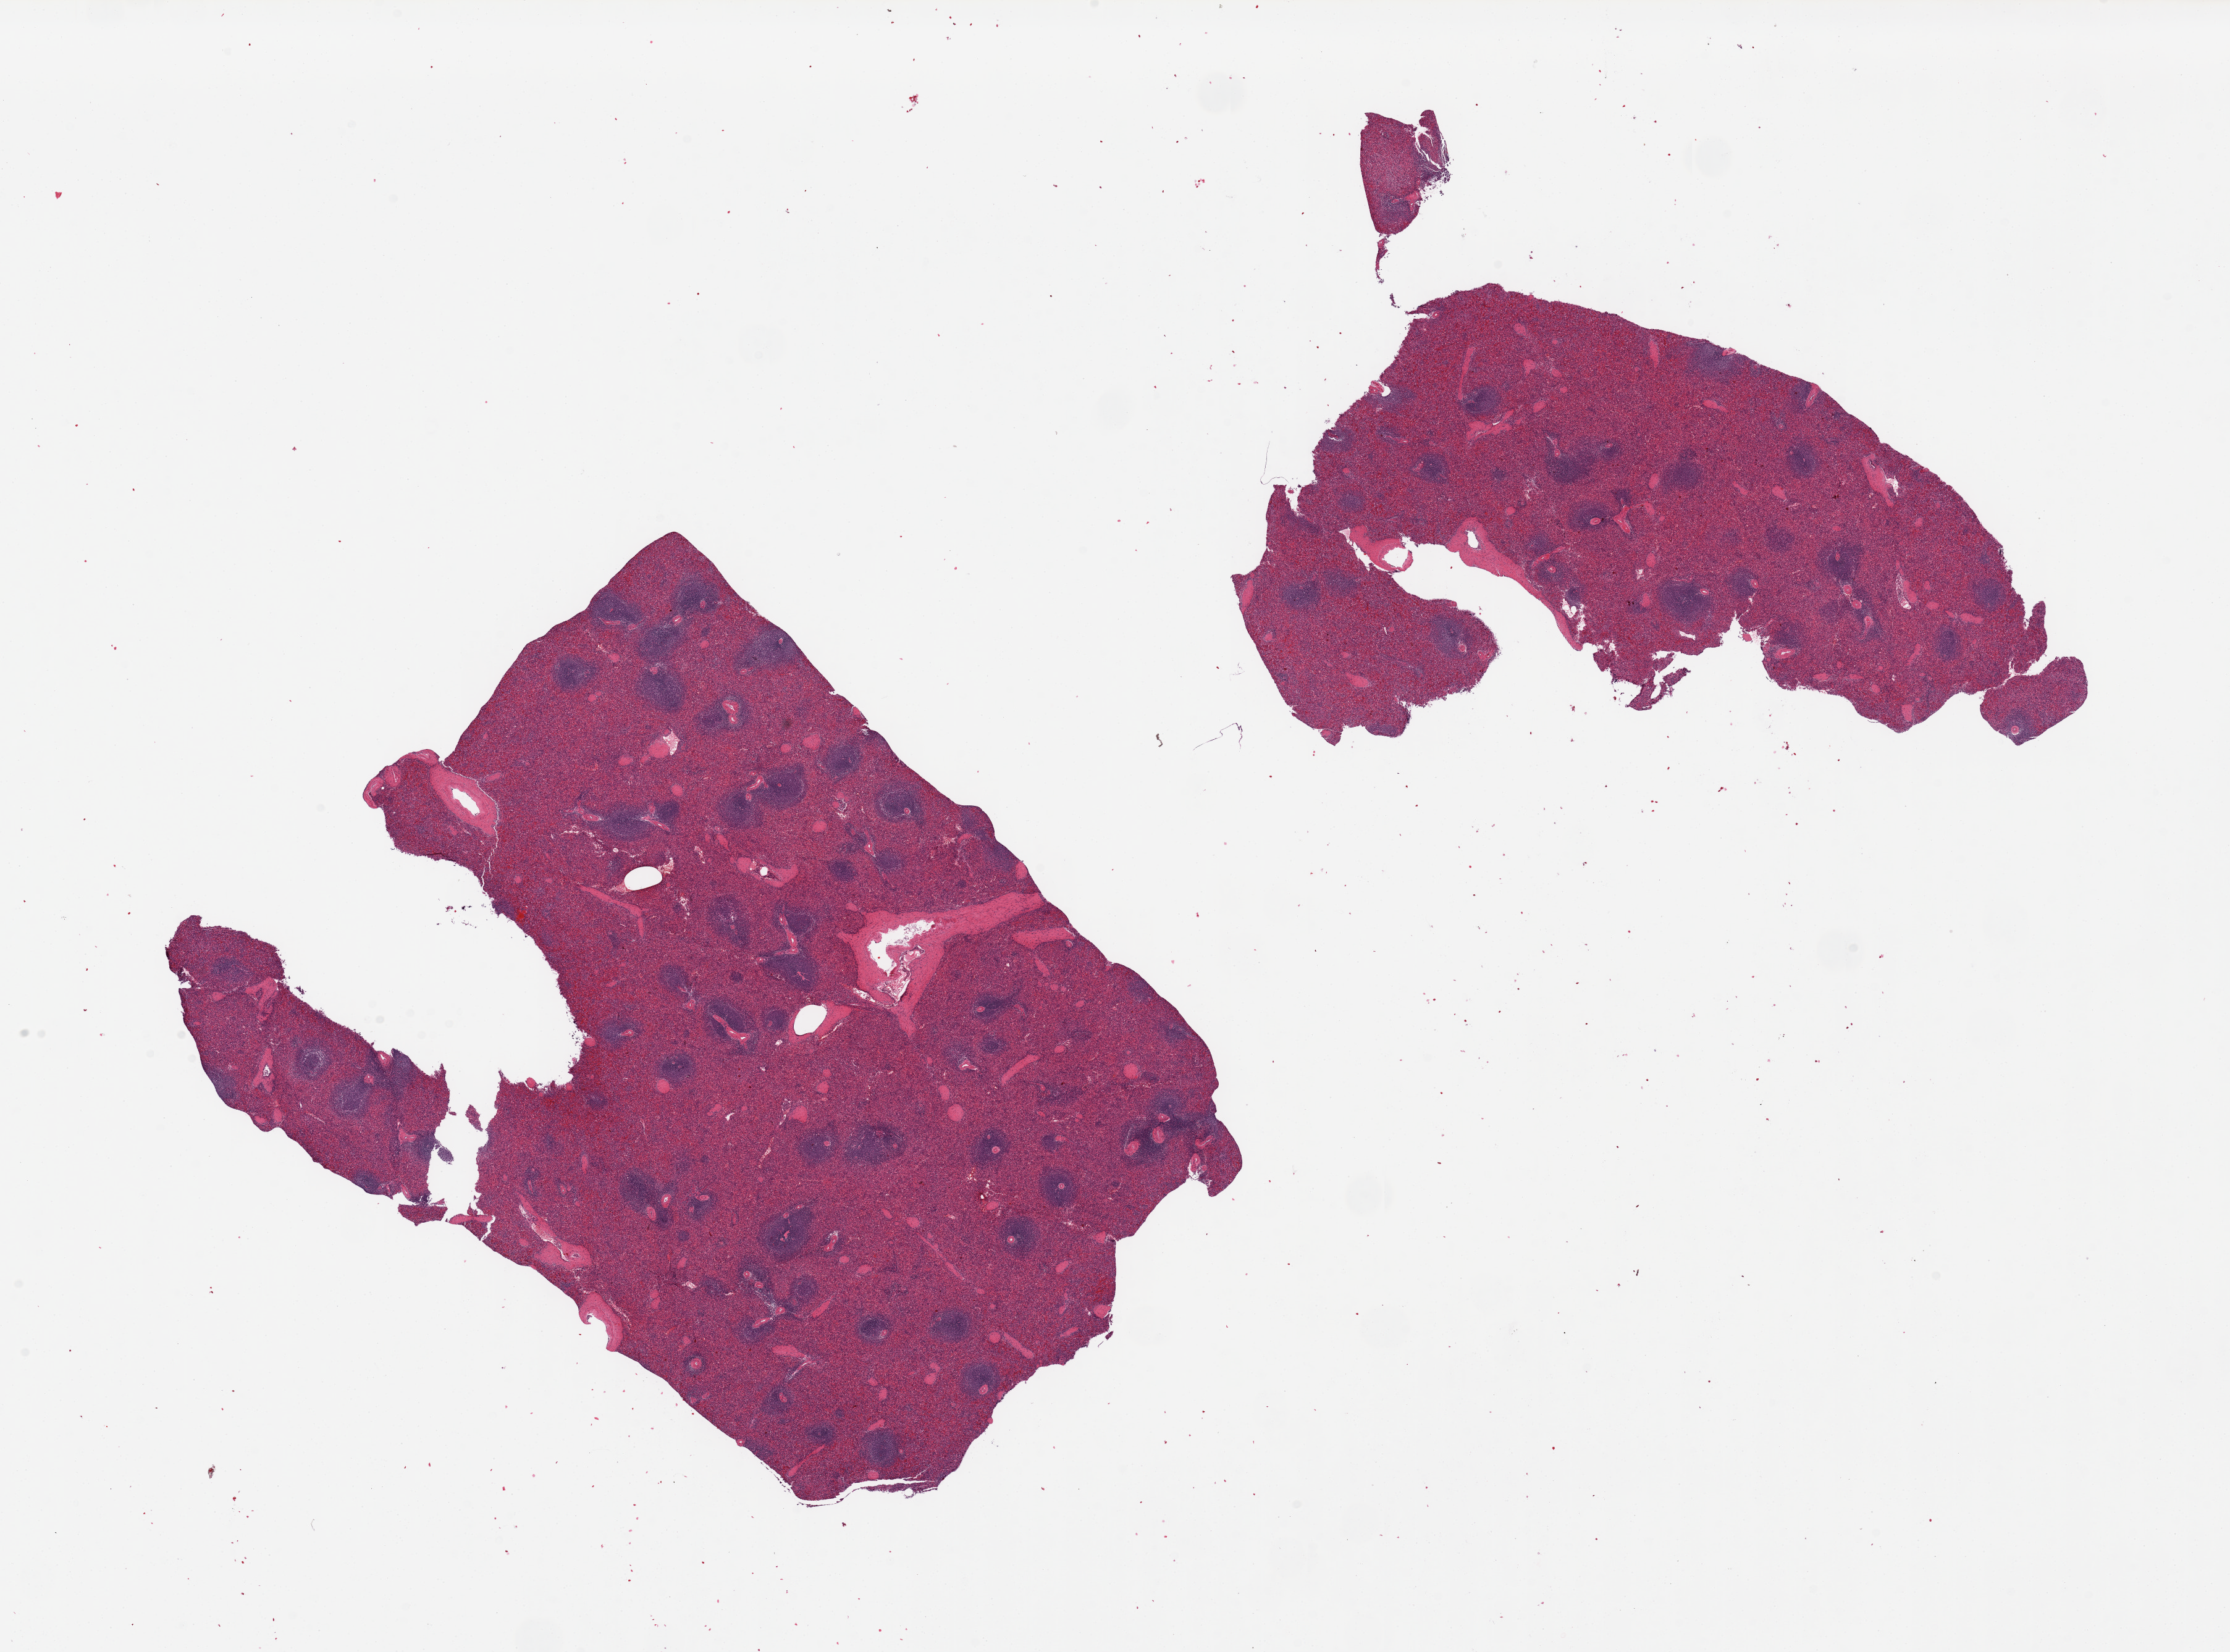
Whole-slide image, haematoxylin and eosin stain — low-resolution overview of the scanned area, about 28.5 x 21.2 mm (slide scanned at 20x); PAXgene-fixed paraffin-embedded (PFPE) section; target tissue: spleen; tissue donor sample. Female donor.
Pathologist's review note for this sample: 2 pieces; slight congestion.